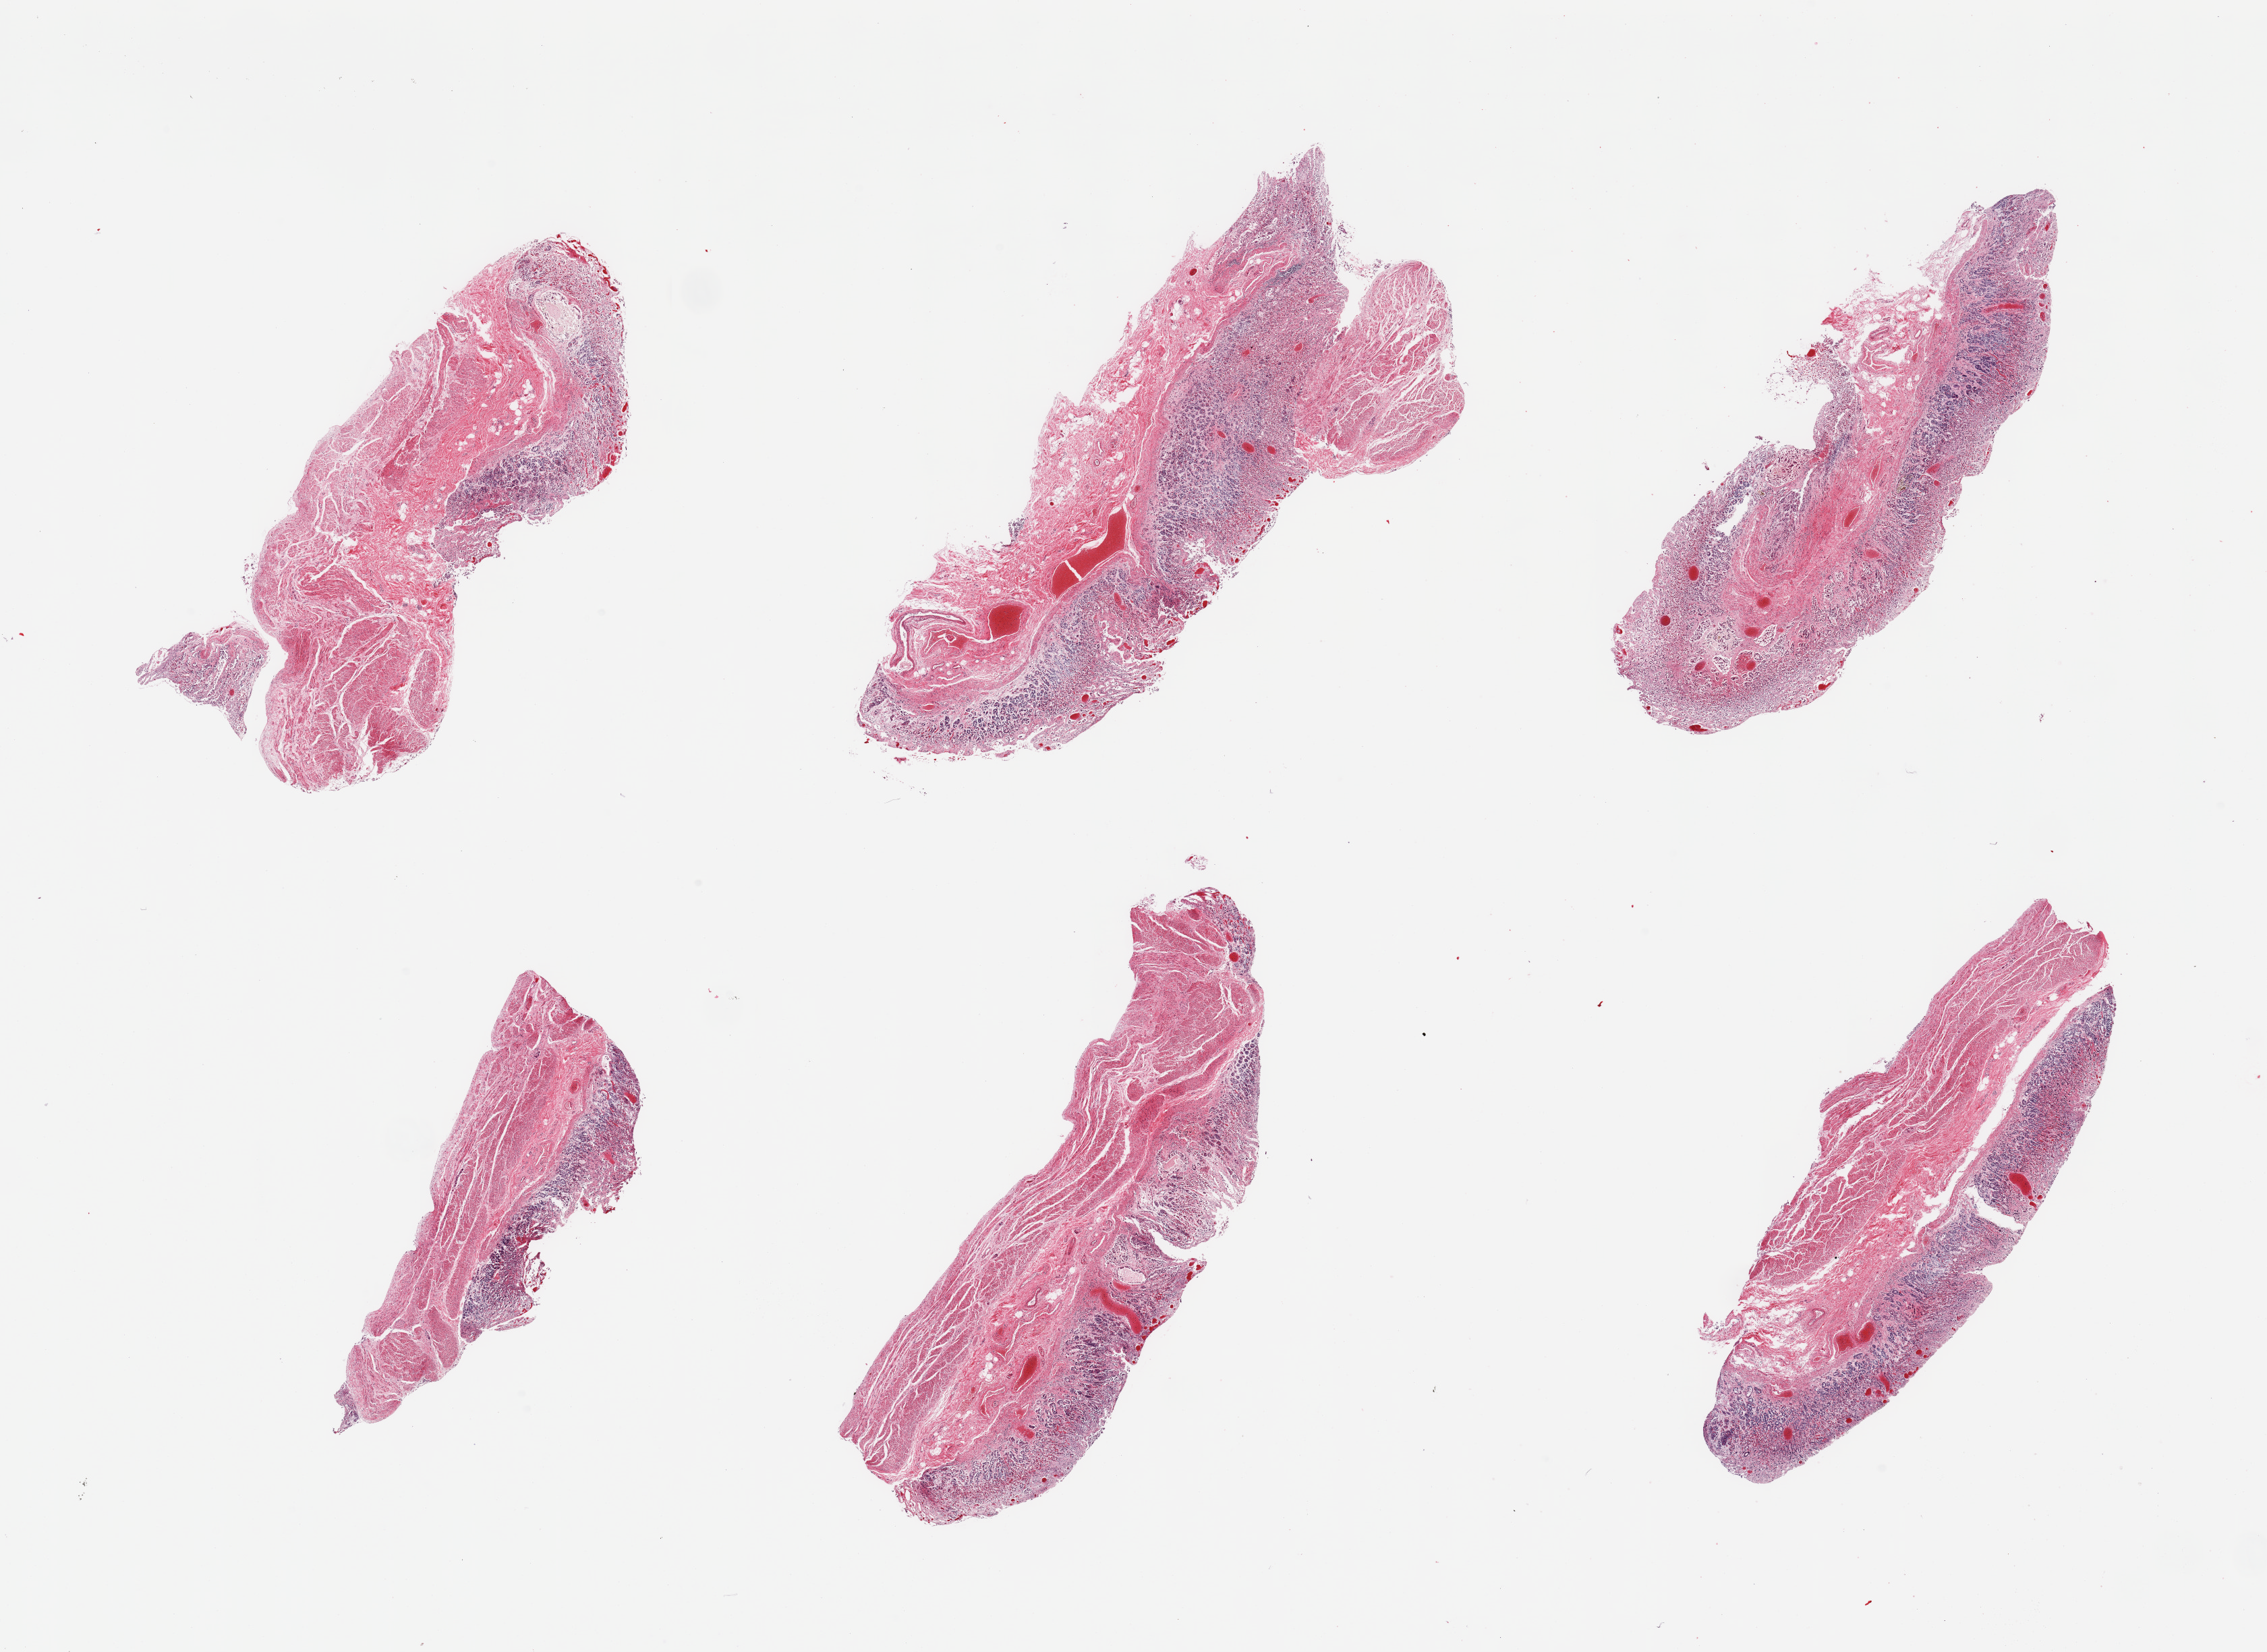
Whole-slide image, hematoxylin and eosin (H&E) stain, low-resolution overview of the scanned area, about 26.6 x 19.4 mm. PAXgene-fixed, paraffin-embedded tissue. Target tissue: stomach. Tissue donor sample. Donor: male.
Review note (as recorded): 6 pieces; moderate to severe mucosal autolysis, muscularis is better preserved.